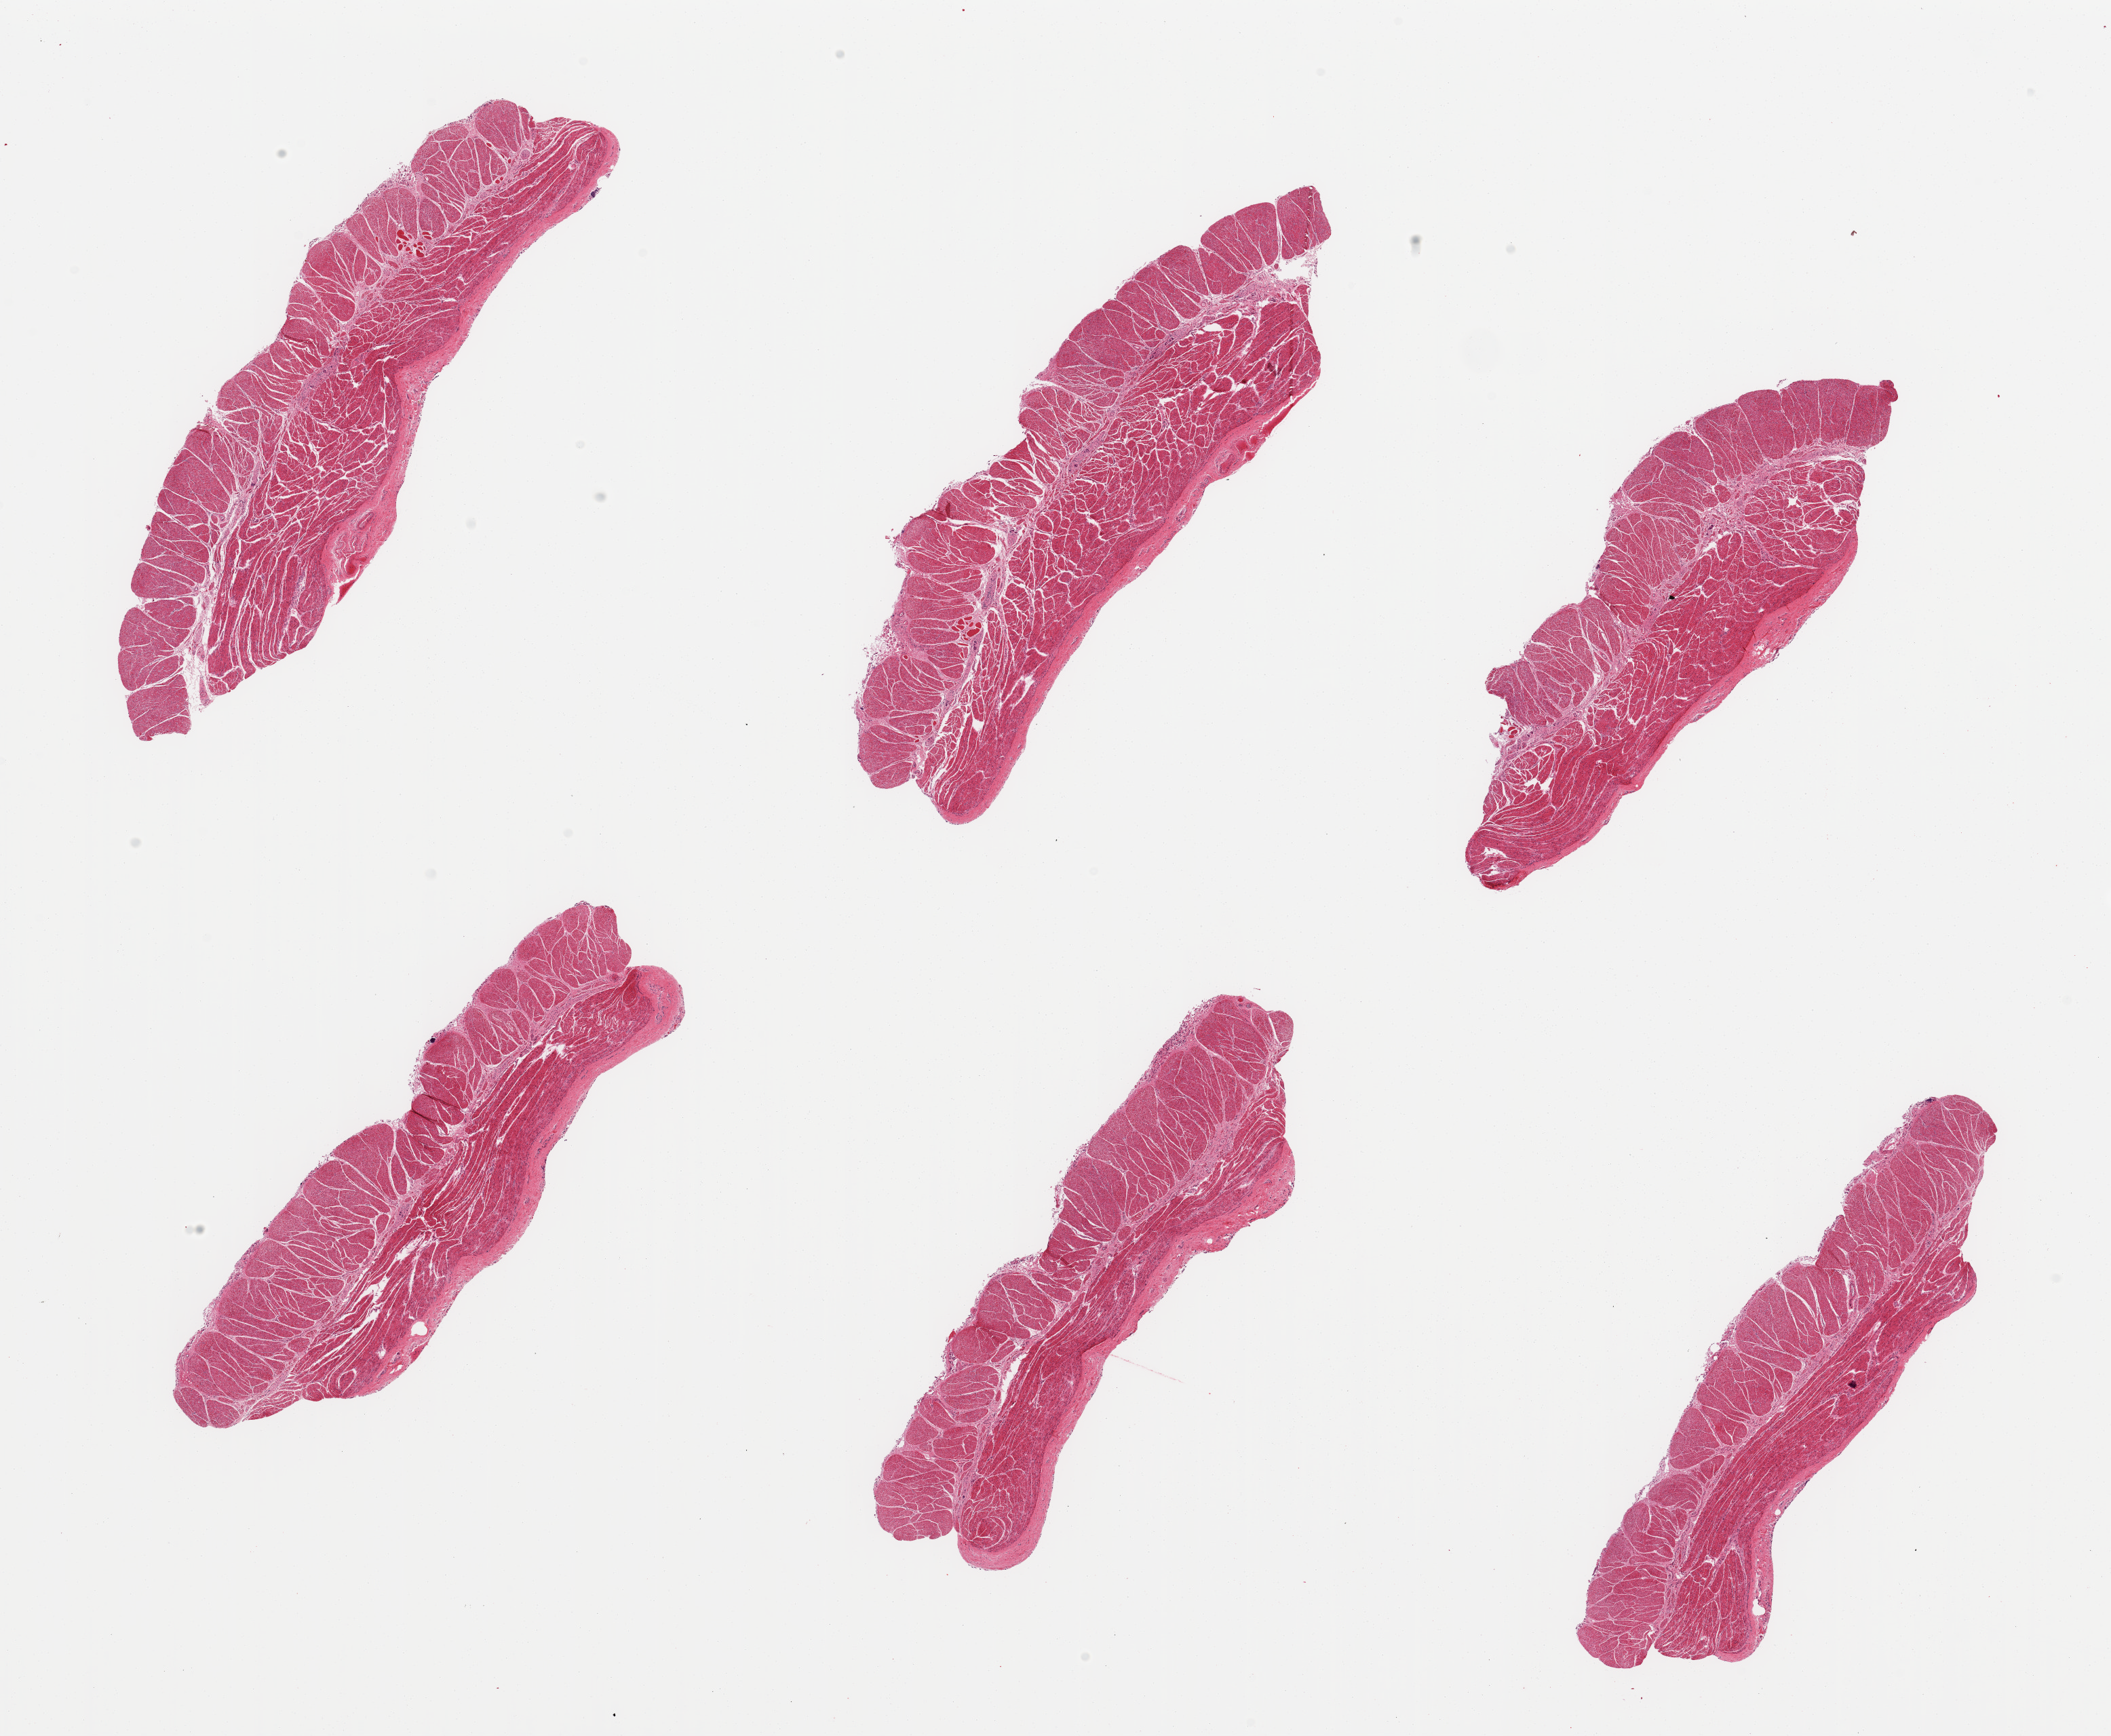
H&E whole-slide image, whole scanned area (about 24.6 x 20.2 mm) shown as a low-resolution overview, PAXgene-fixed, paraffin-embedded tissue, sampled site (target tissue): esophageal muscle, donor tissue sample.
Pathologist's review note for this sample: 6 pieces, confirmed target muscularis.